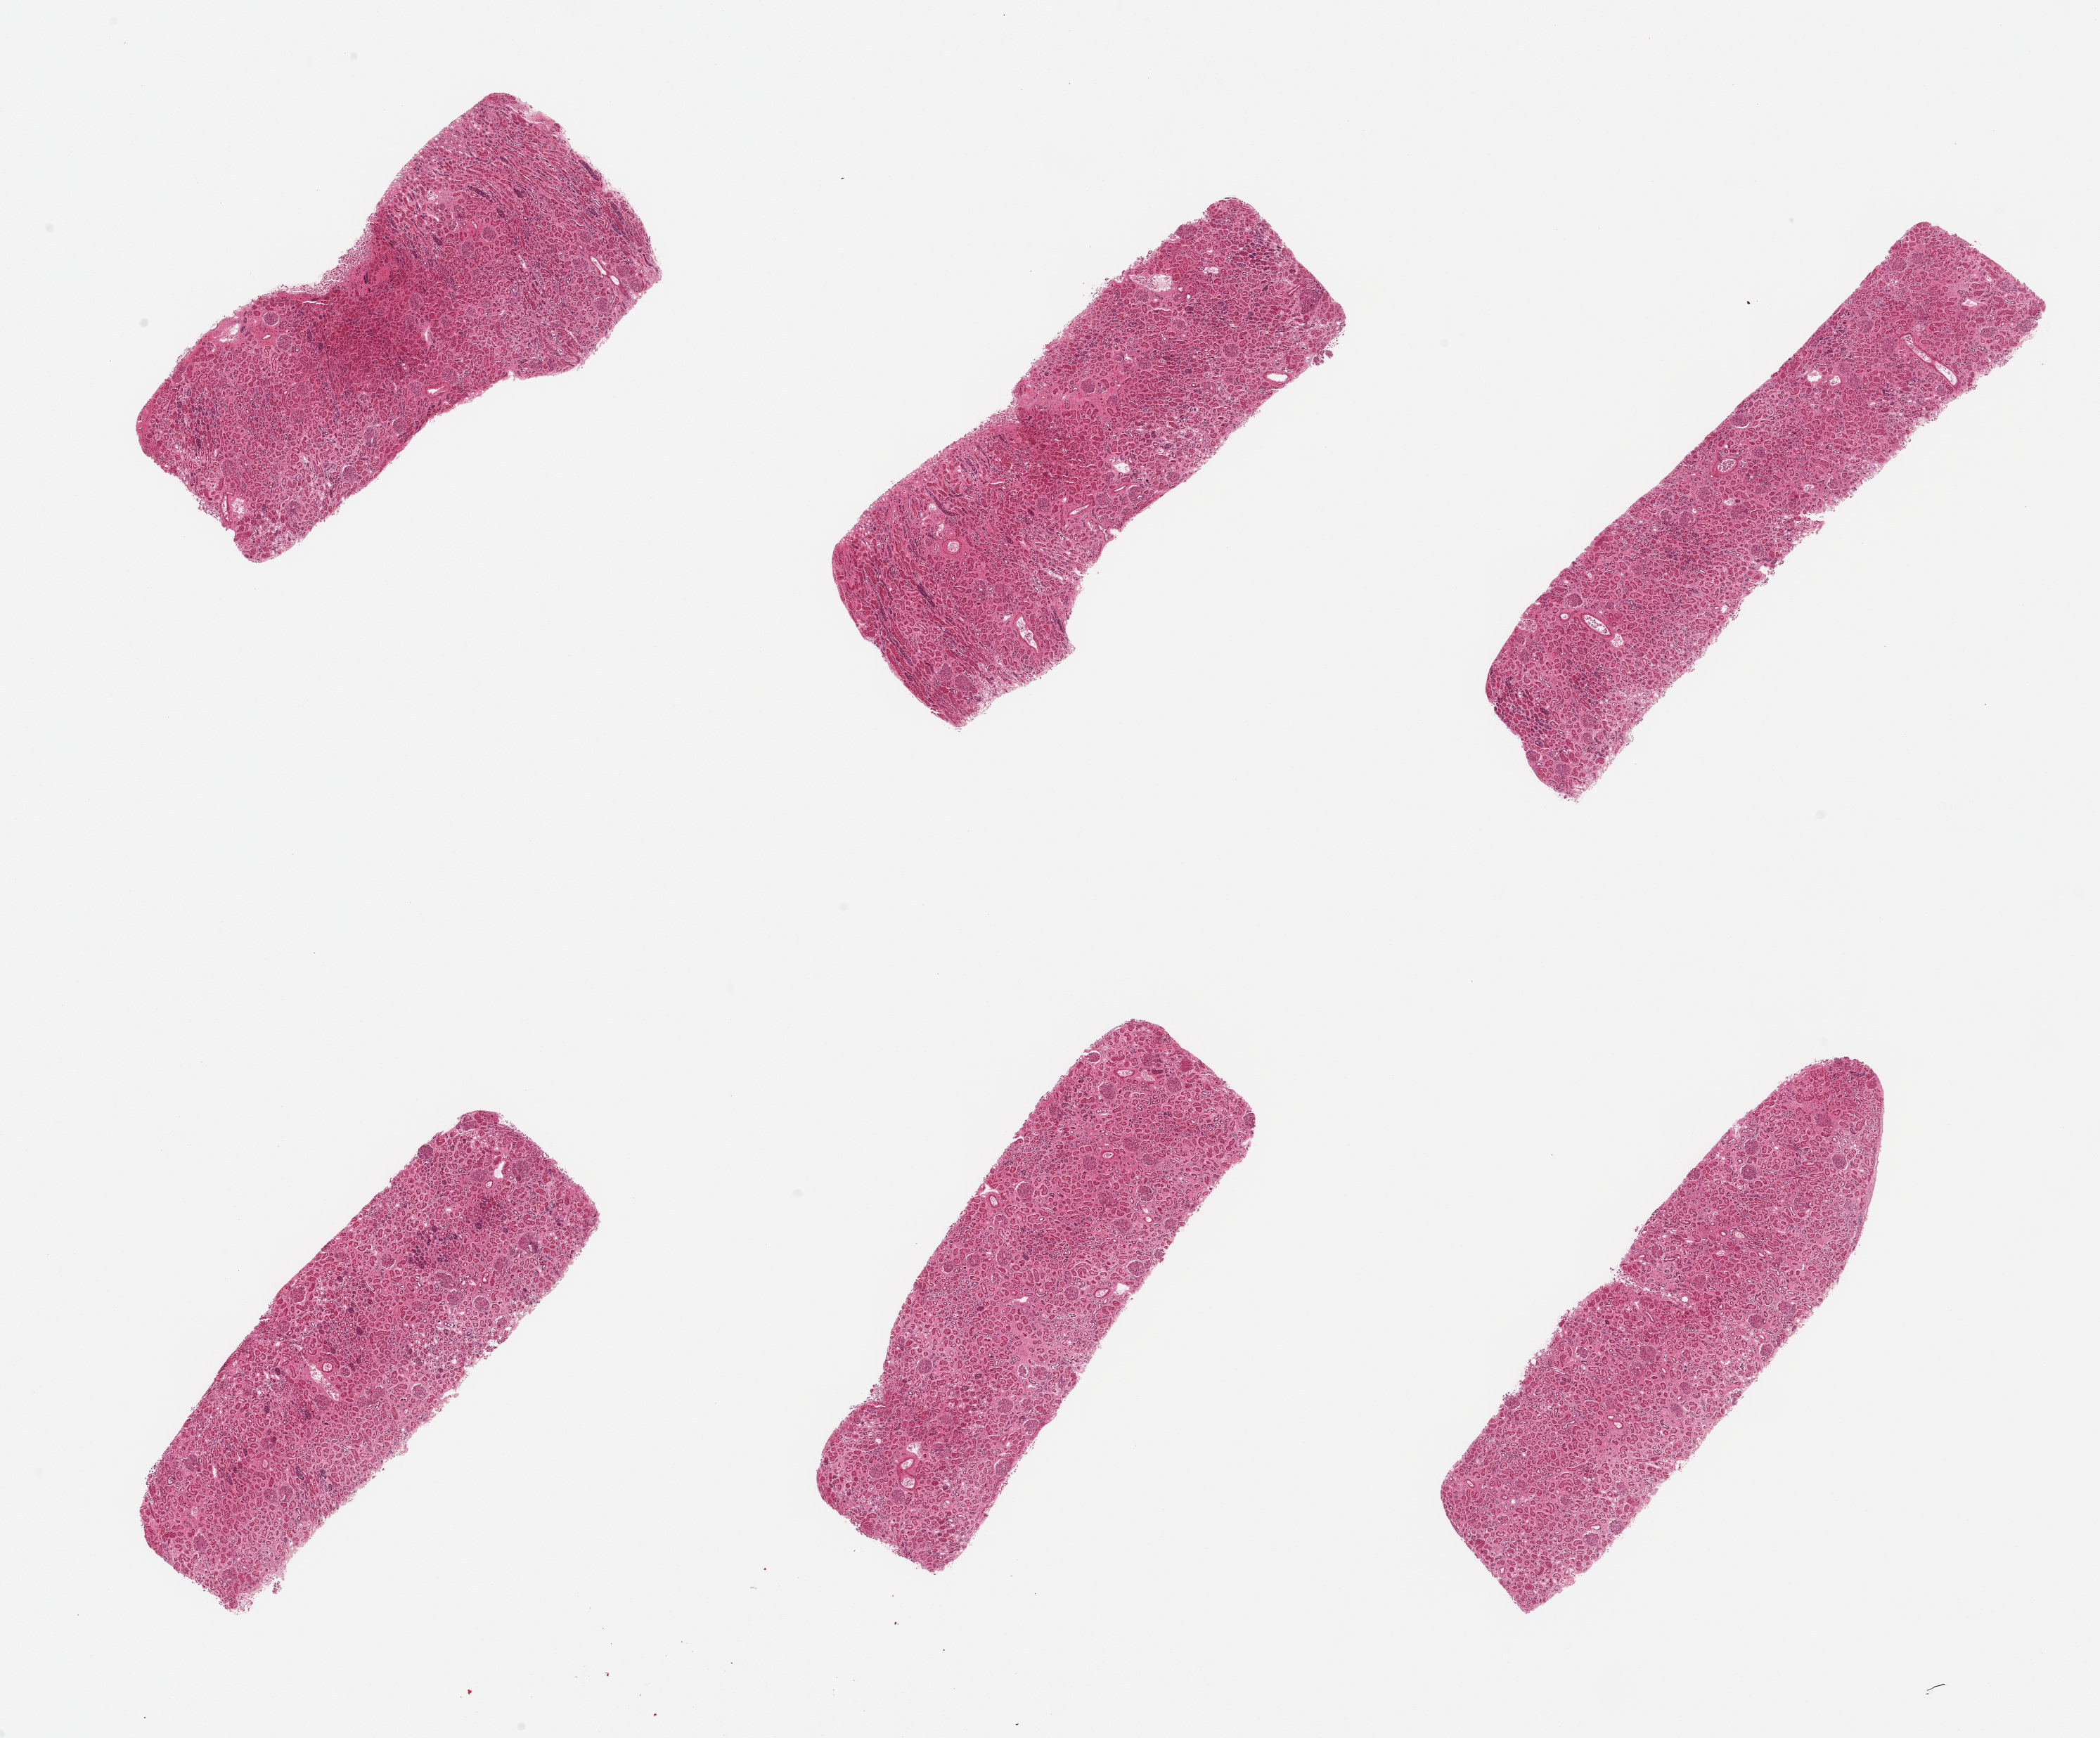
Digitized H&E-stained section, brightfield — a low-resolution overview of the entire scanned area, about 23.6 x 19.6 mm (slide scanned at 20x), PAXgene-fixed, paraffin-embedded tissue, sampled site (target tissue): renal cortex, tissue donor sample.
* review note (as recorded): 6 pieces, glomeruli present; tubules autolyzed